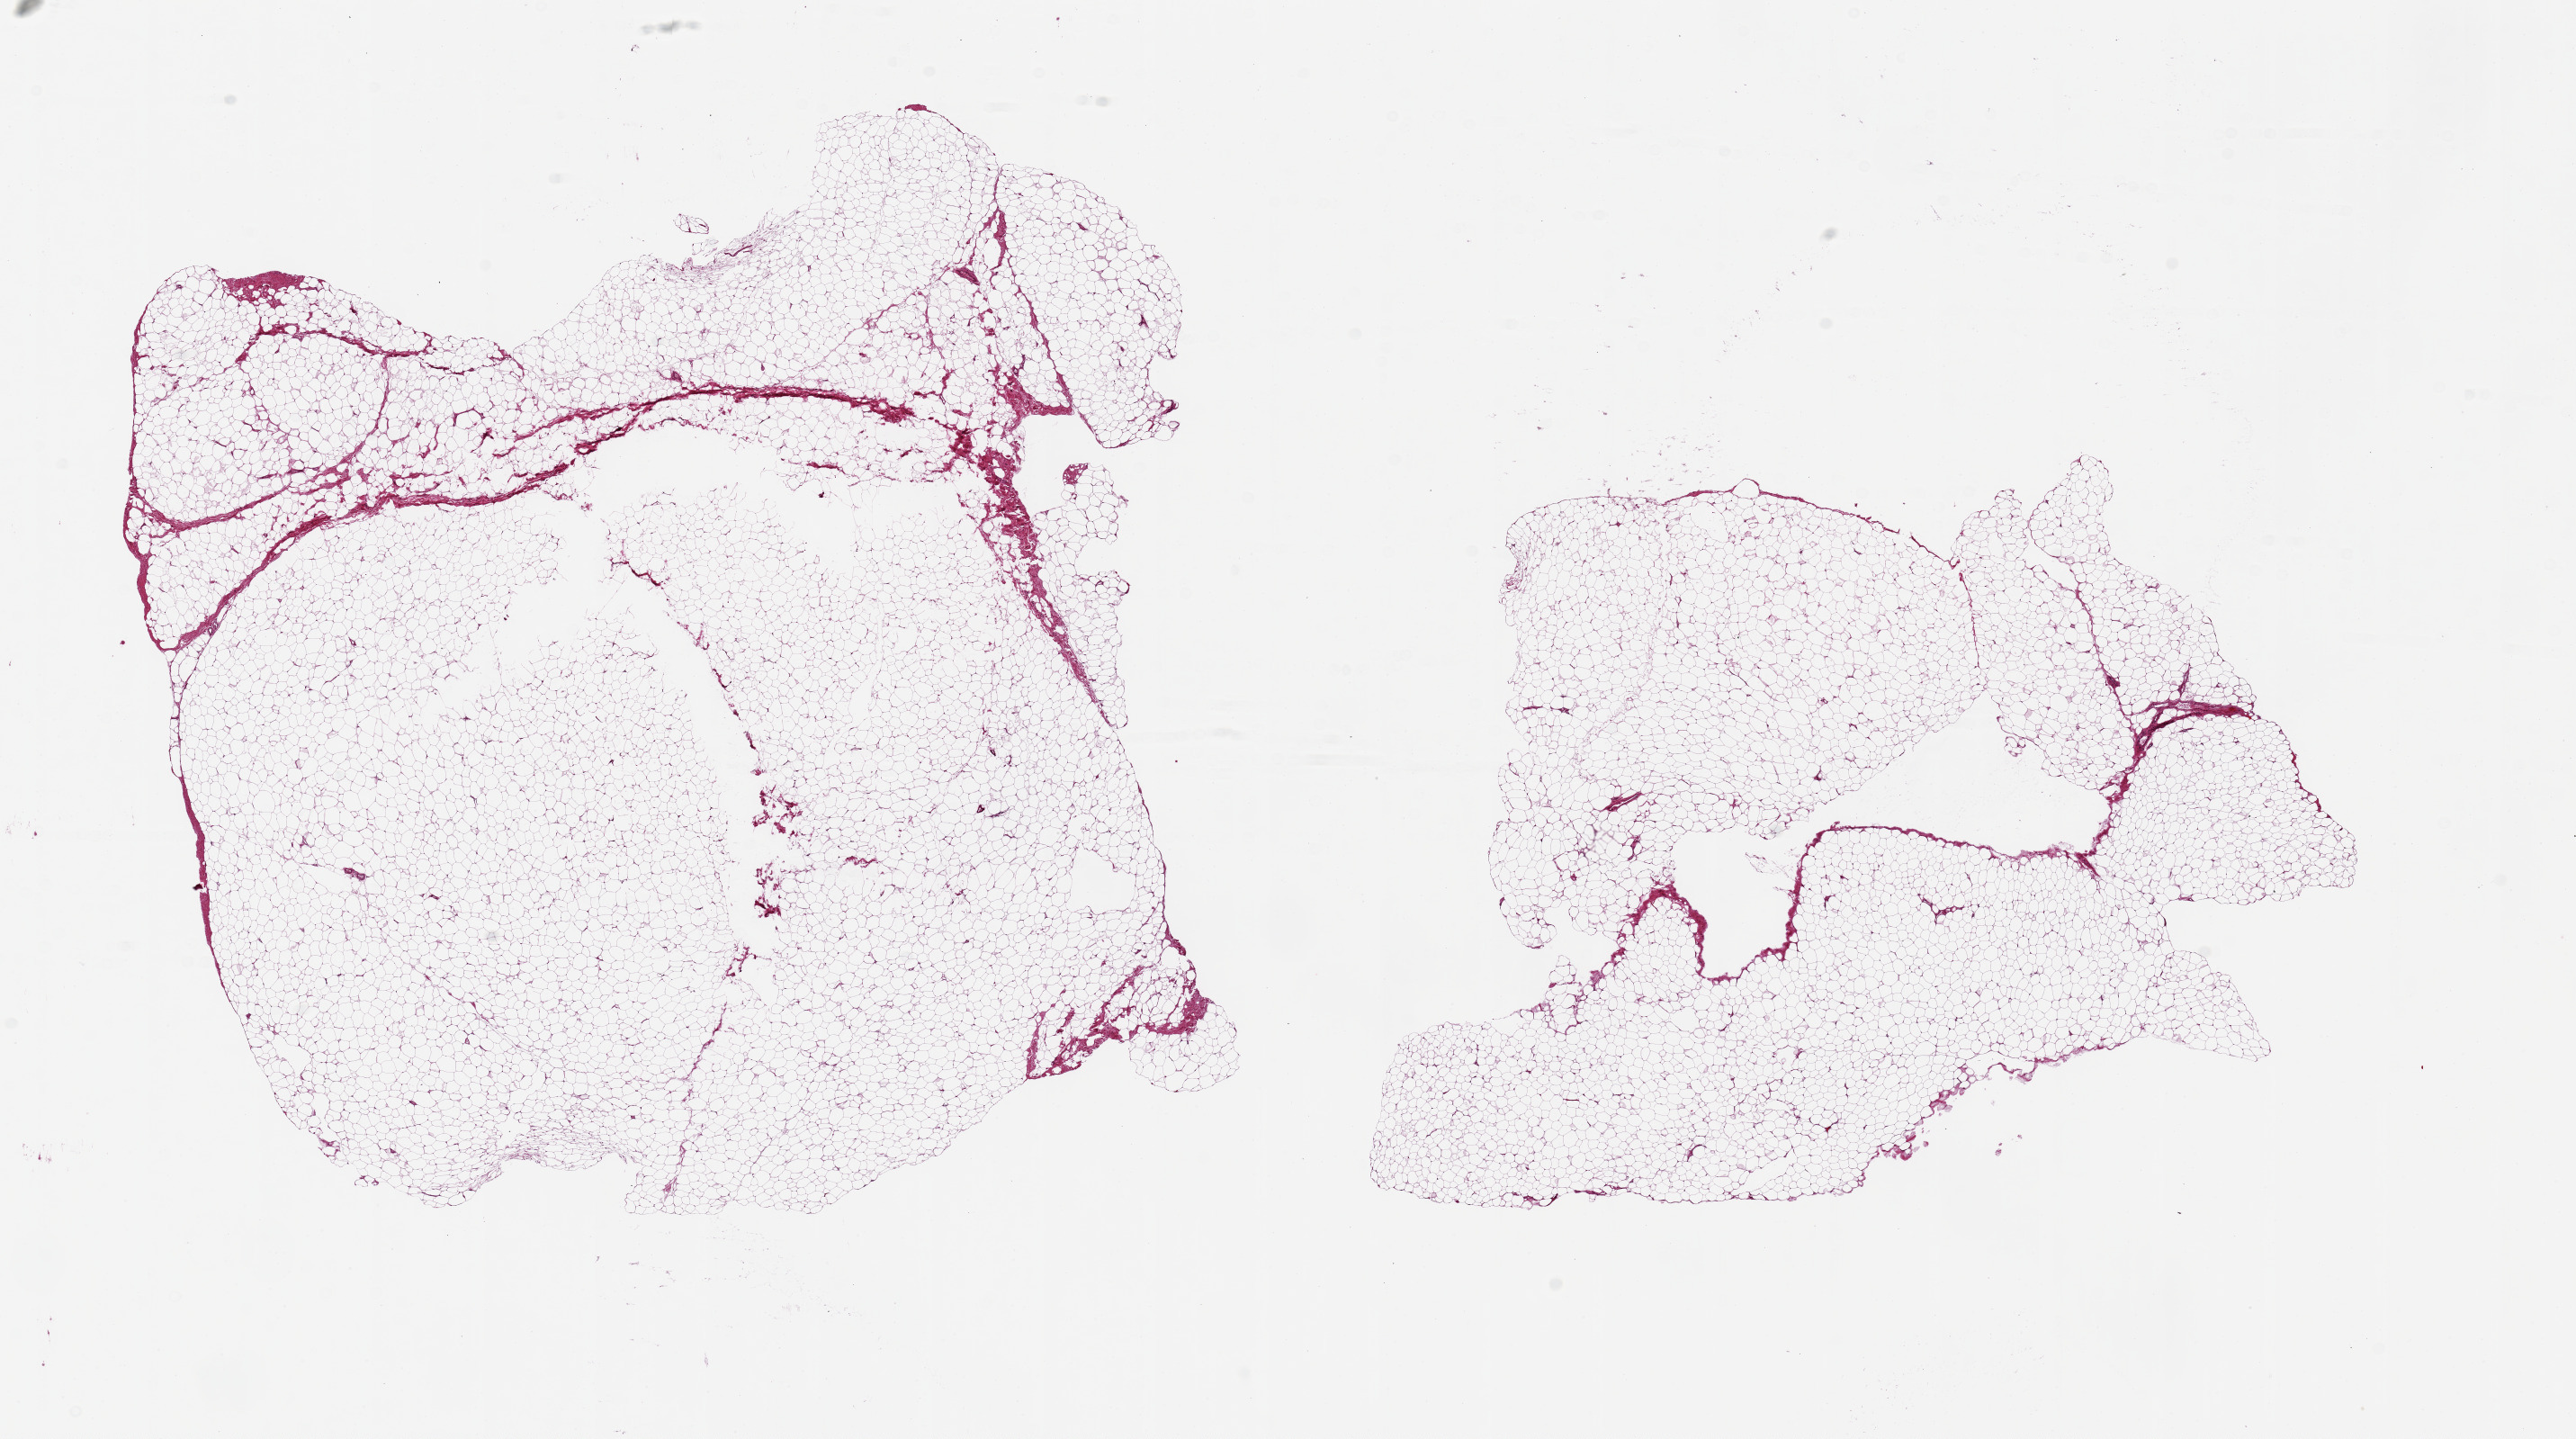
Digitized haematoxylin and eosin-stained section — a low-resolution overview of the entire scanned area, about 22.6 x 12.6 mm. PAXgene-fixed paraffin-embedded (PFPE) section. Section of breast (target tissue). Tissue donor sample. Male donor.
* reviewer comment on this tissue sample: 2 pieces 10x9 & 9x7mm; no ductal elements, all fibroadipose tissue